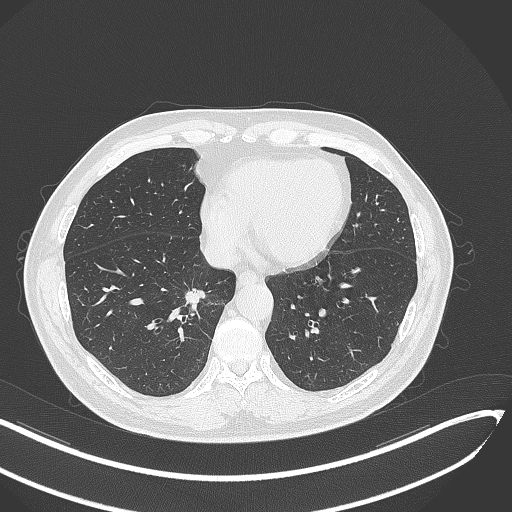
Chest CT, one axial slice; slice 127 of 429 in the series (ordered by position); reconstruction kernel B70f; lung window (W 1500 / L -600 HU); 512 × 512 image matrix. Male patient, age 62 years. Case-level facts recorded for this patient, not image findings: clinical TNM (as recorded): T1b N0 M0.
Annotated regions visible in this slice (rectangle marked by the reading radiologist):
- lung tumour (recorded histology: adenocarcinoma): bounding box [x1, y1, x2, y2] px = [177, 282, 213, 308]